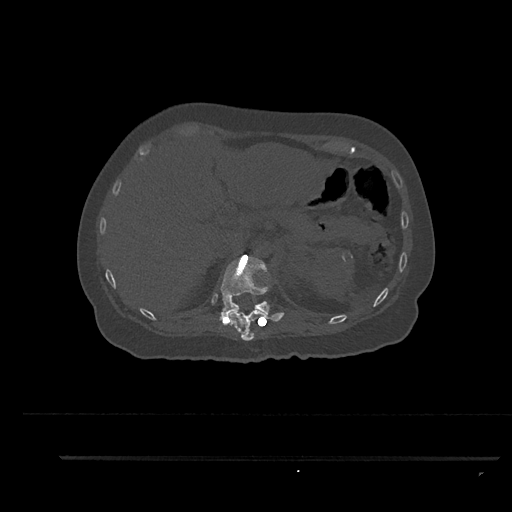
CT including the spine, one axial slice. Position 286 of 797 along the scan axis. 120 kVp. Bone window (W 1800 / L 400 HU). 0.5 mm slice thickness. 512 × 512 image matrix, field of view 408 × 408 mm. Patient: female, 44 years. Case-level facts recorded for this patient, not image findings: primary cancer: renal; vertebrae with lytic lesions (as recorded): L1.
Annotated regions visible in this slice (semi-automatically segmented with operator editing):
- T11 vertebra: bounding box [x1, y1, x2, y2] px = [232, 308, 264, 341]
- T12 vertebra: [220, 256, 284, 322]